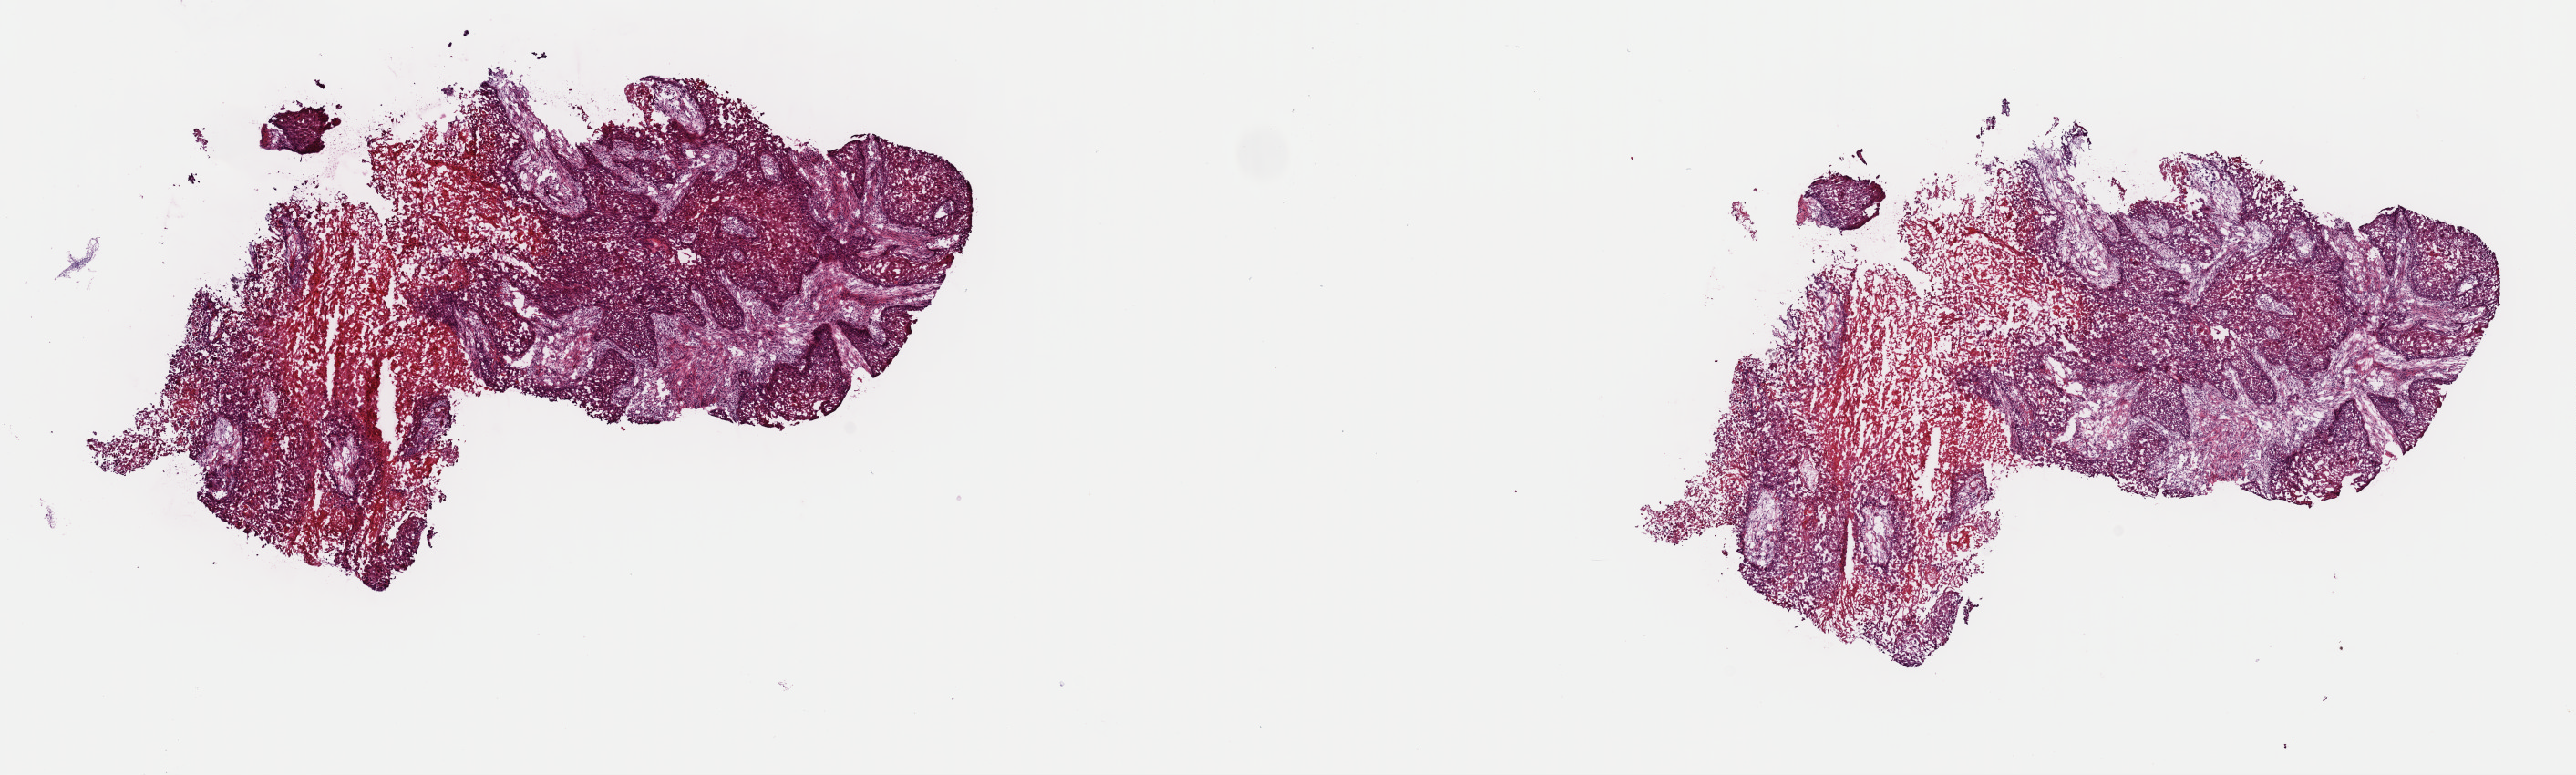
H&E whole-slide image, whole scanned area (about 22.3 x 6.7 mm, acquisition: 40x scan) shown as a low-resolution overview; frozen section from the top of the tissue portion; head and neck, primary tumour sample. Female patient; age at initial diagnosis 47 years.
Diagnosis: Squamous cell carcinoma, NOS (floor of mouth, NOS).